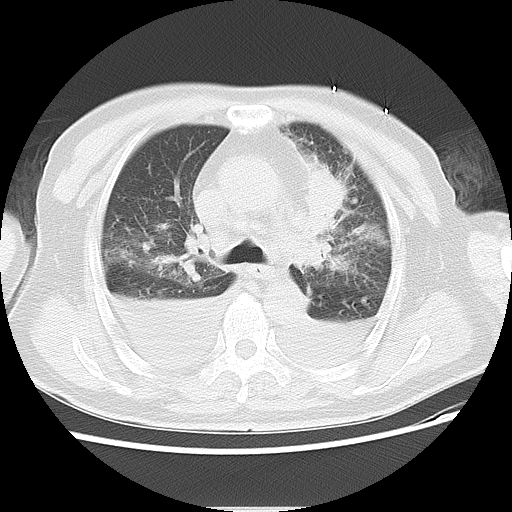
Chest CT, one axial slice. Slice 16 of 22 in the series (ordered by position). Reconstruction kernel LUNG. 120 kVp. Lung window (W 1500 / L -600 HU). 5 mm slice thickness. 512 × 512 image matrix, field of view 350 × 350 mm. Patient: male, 66 years. Case-level facts recorded for this patient, not image findings: clinical TNM (as recorded): T1c N0 M0.
Annotated regions visible in this slice (bounding box drawn by a radiologist):
- lung tumour (recorded histology: adenocarcinoma): box from (x=300, y=155) to (x=349, y=236) px